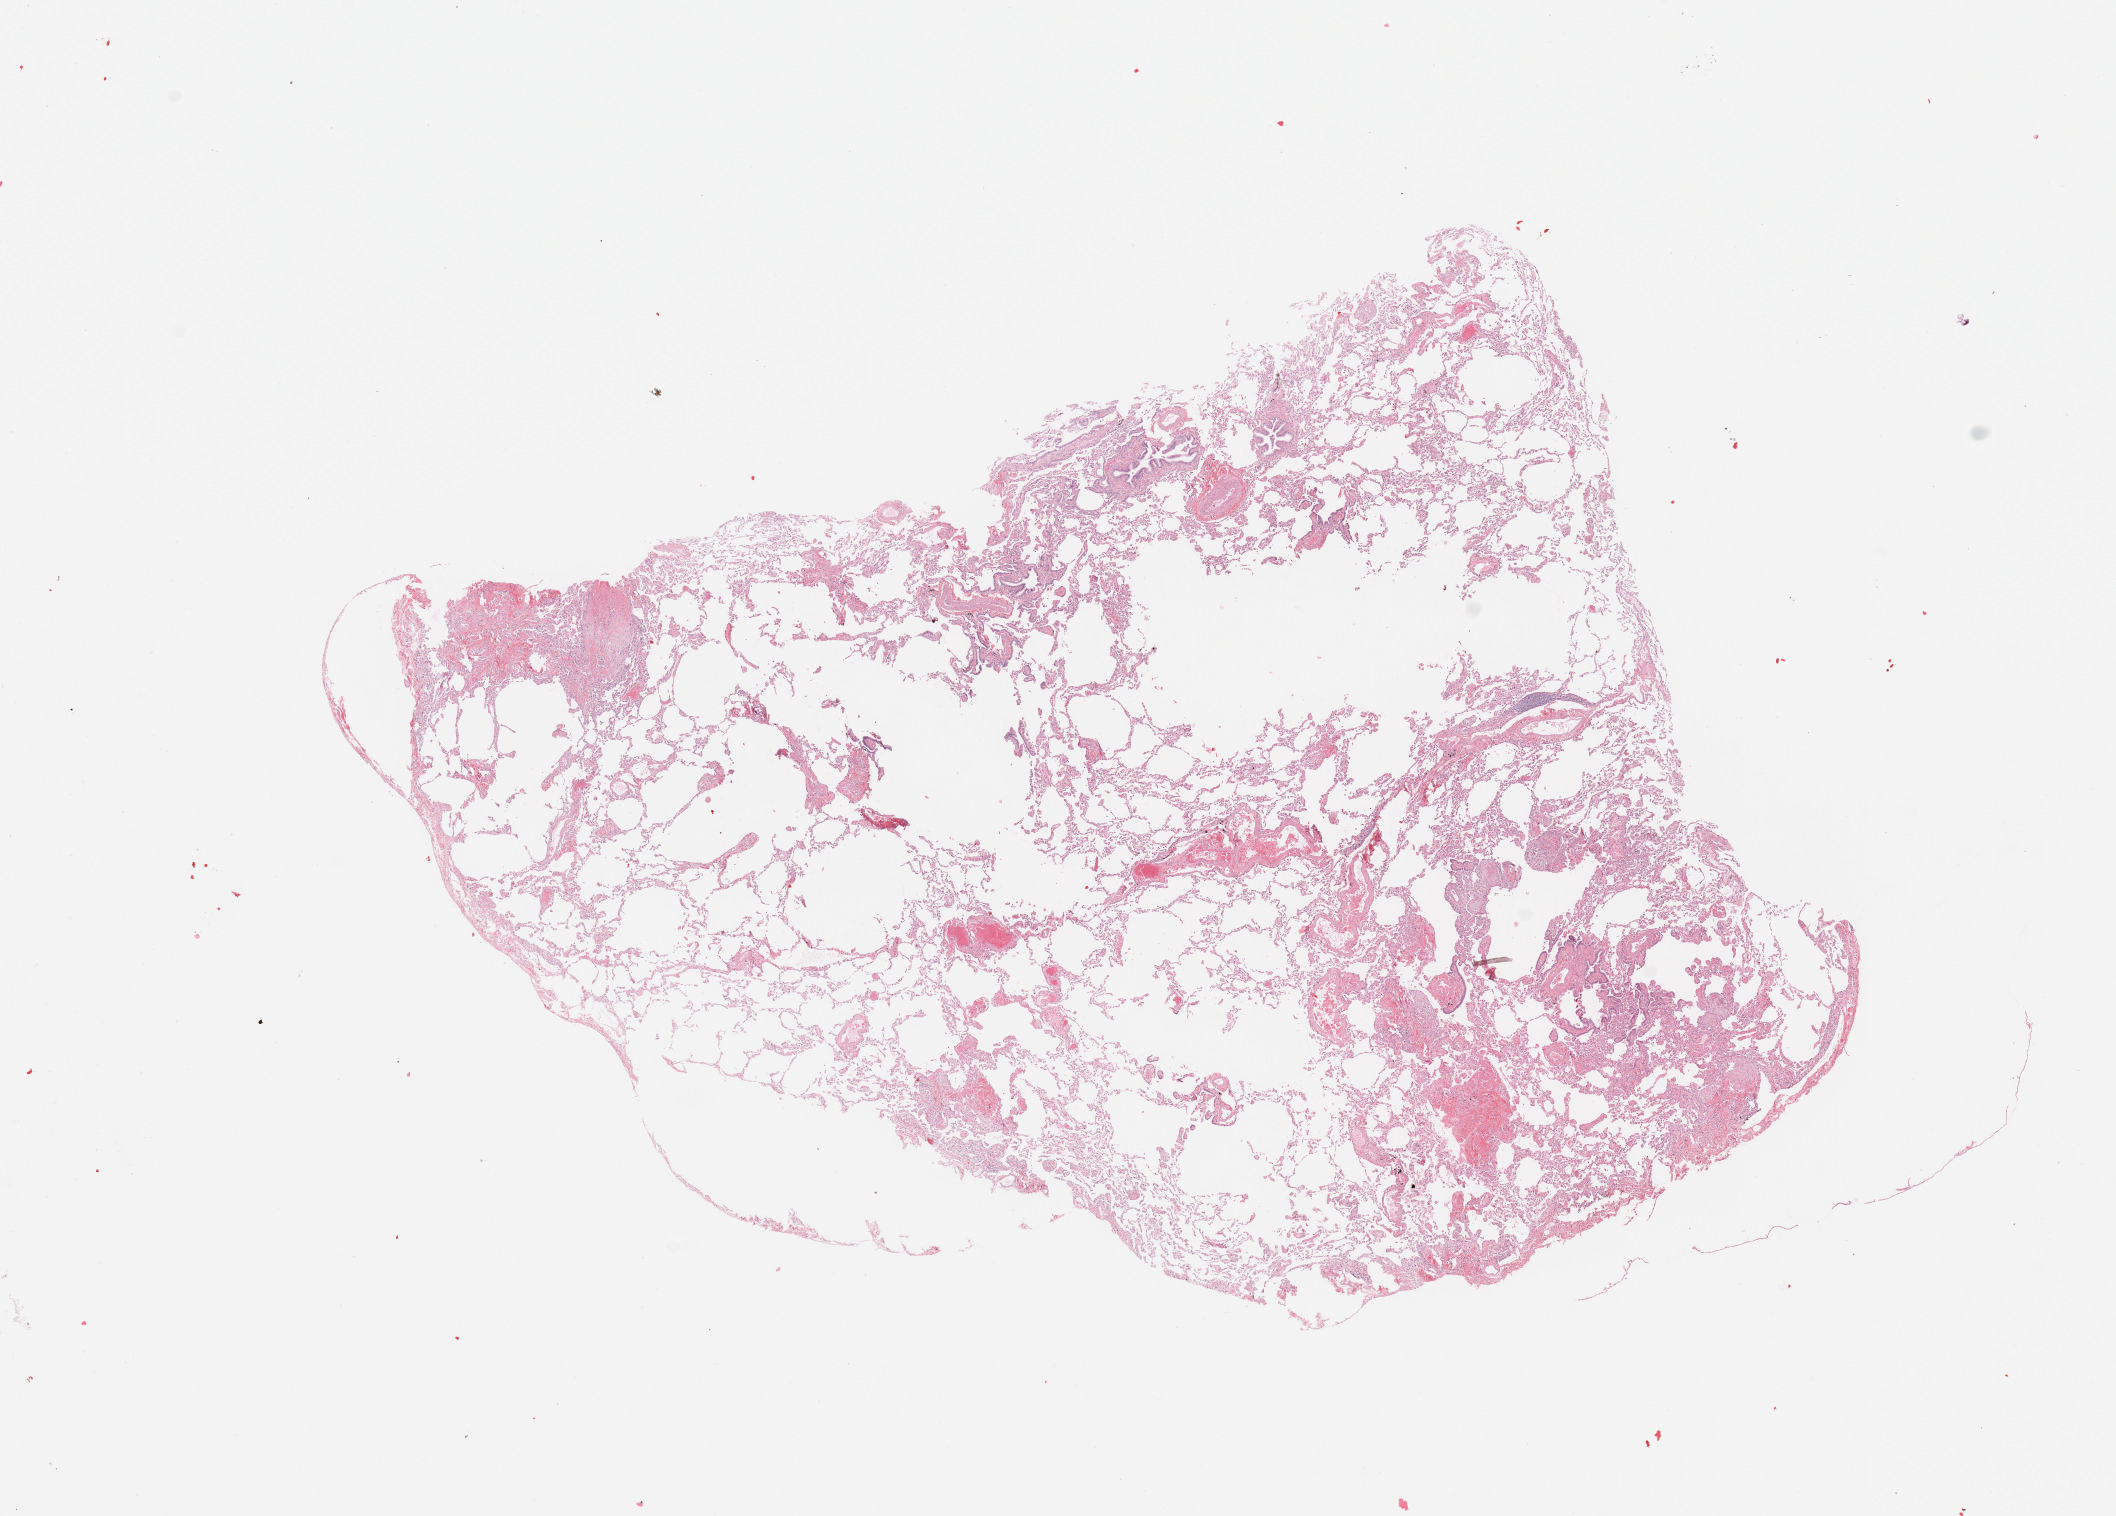
Whole-slide histology image, Hematoxylin and eosin (H&E) stained, whole scanned area (about 16.7 x 12.0 mm, acquisition: 20x scan) shown as a low-resolution overview. Normal (non-tumour) tissue sample, sampled site: lung. Male, 53 y/o.
This section: normal (non-tumour) tissue from the same patient. Patient diagnosis: Squamous cell carcinoma, NOS.